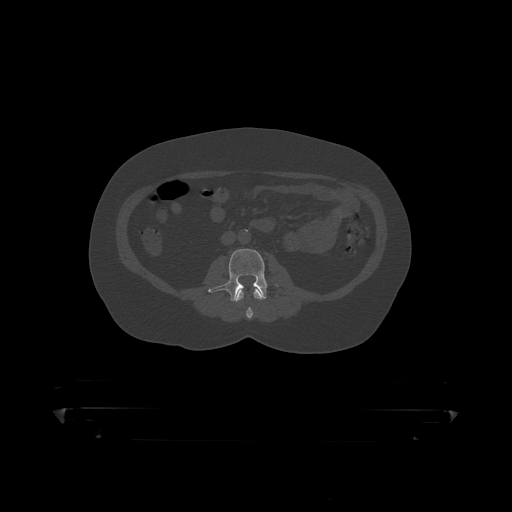
CT including the spine, one axial slice; slice 97 of 390 in the series (ordered by position); reconstruction kernel STANDARD; 120 kVp; bone window (W 1800 / L 400 HU); 512 × 512 image matrix, field of view 650 × 650 mm. Patient: male, 60 years. Case-level facts recorded for this patient, not image findings: primary cancer: prostate.
Annotated regions visible in this slice (semi-automatically segmented with operator editing):
- L2 vertebra: bounding box <236,289,264,319> (left, top, right, bottom; pixels)
- L3 vertebra: <209,249,267,302>